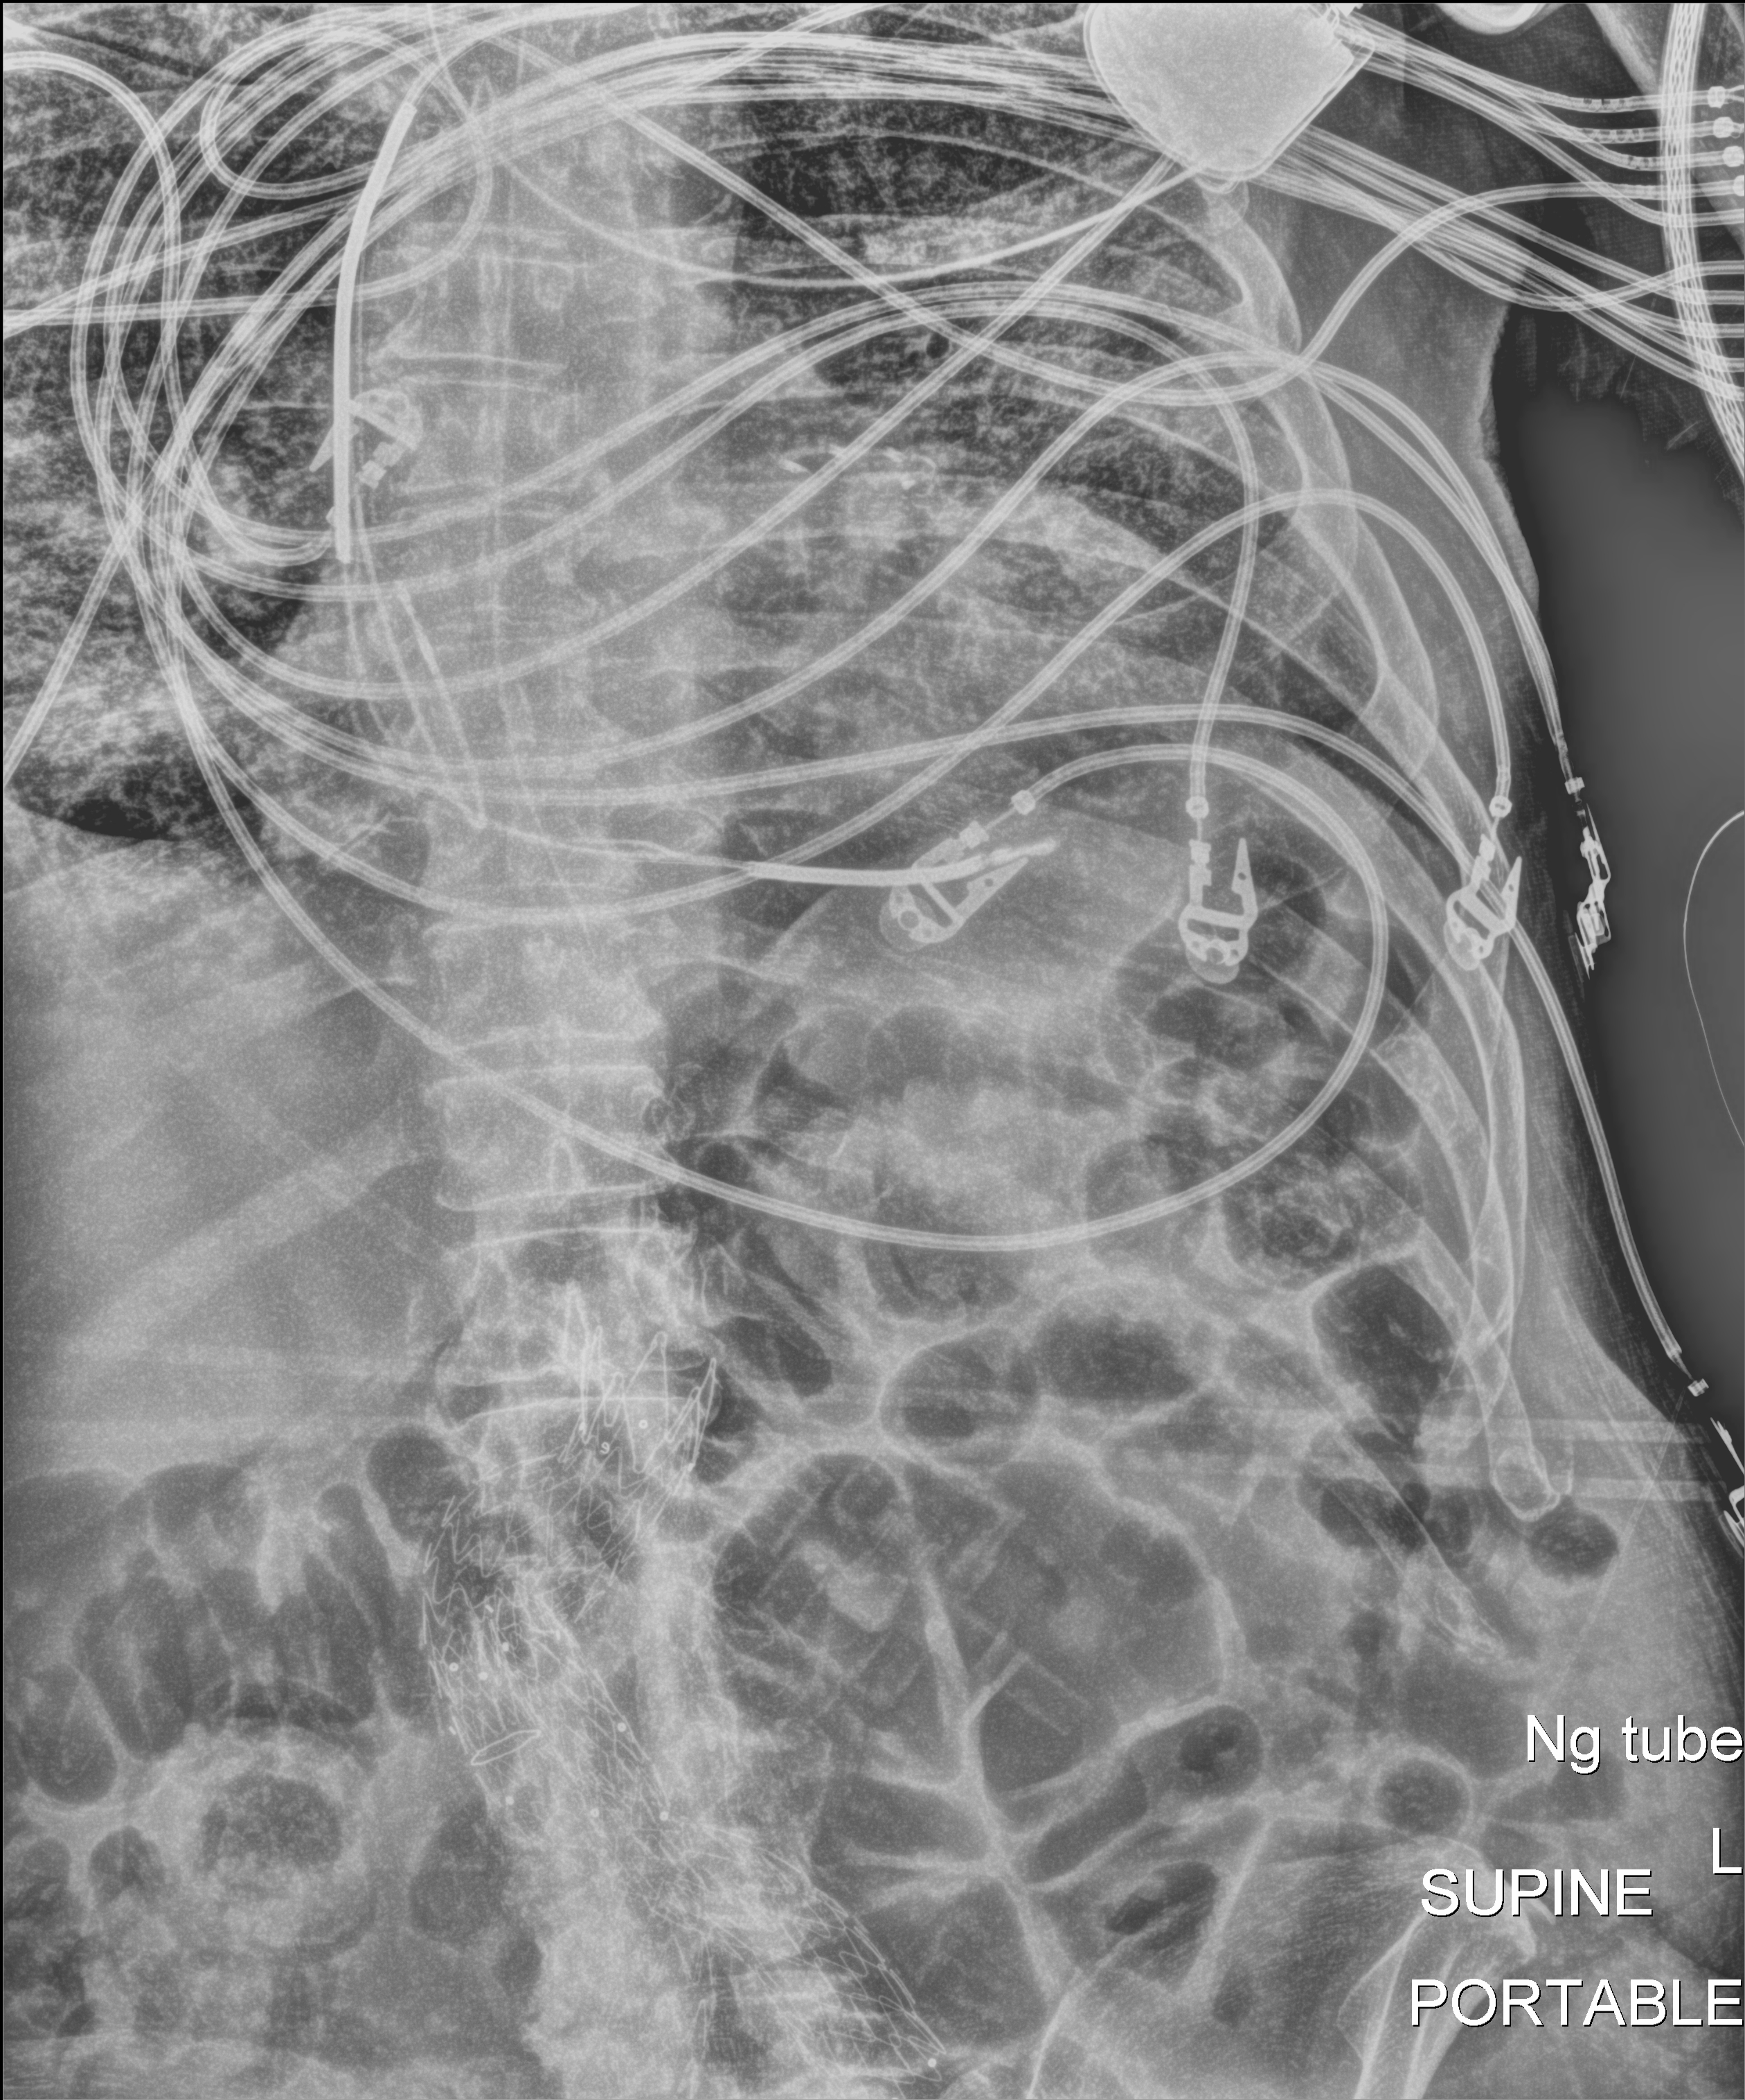
Portable abdomen radiograph; anteroposterior (AP) projection. Patient hospitalised with COVID-19; male, aged 60–74 years.
Admission-level facts for this patient (not findings on this image; timing relative to this image not recorded):
- mechanically ventilated during this hospital stay: yes
- admitted to intensive care during this hospital stay: yes
- smoking status (admission record): former